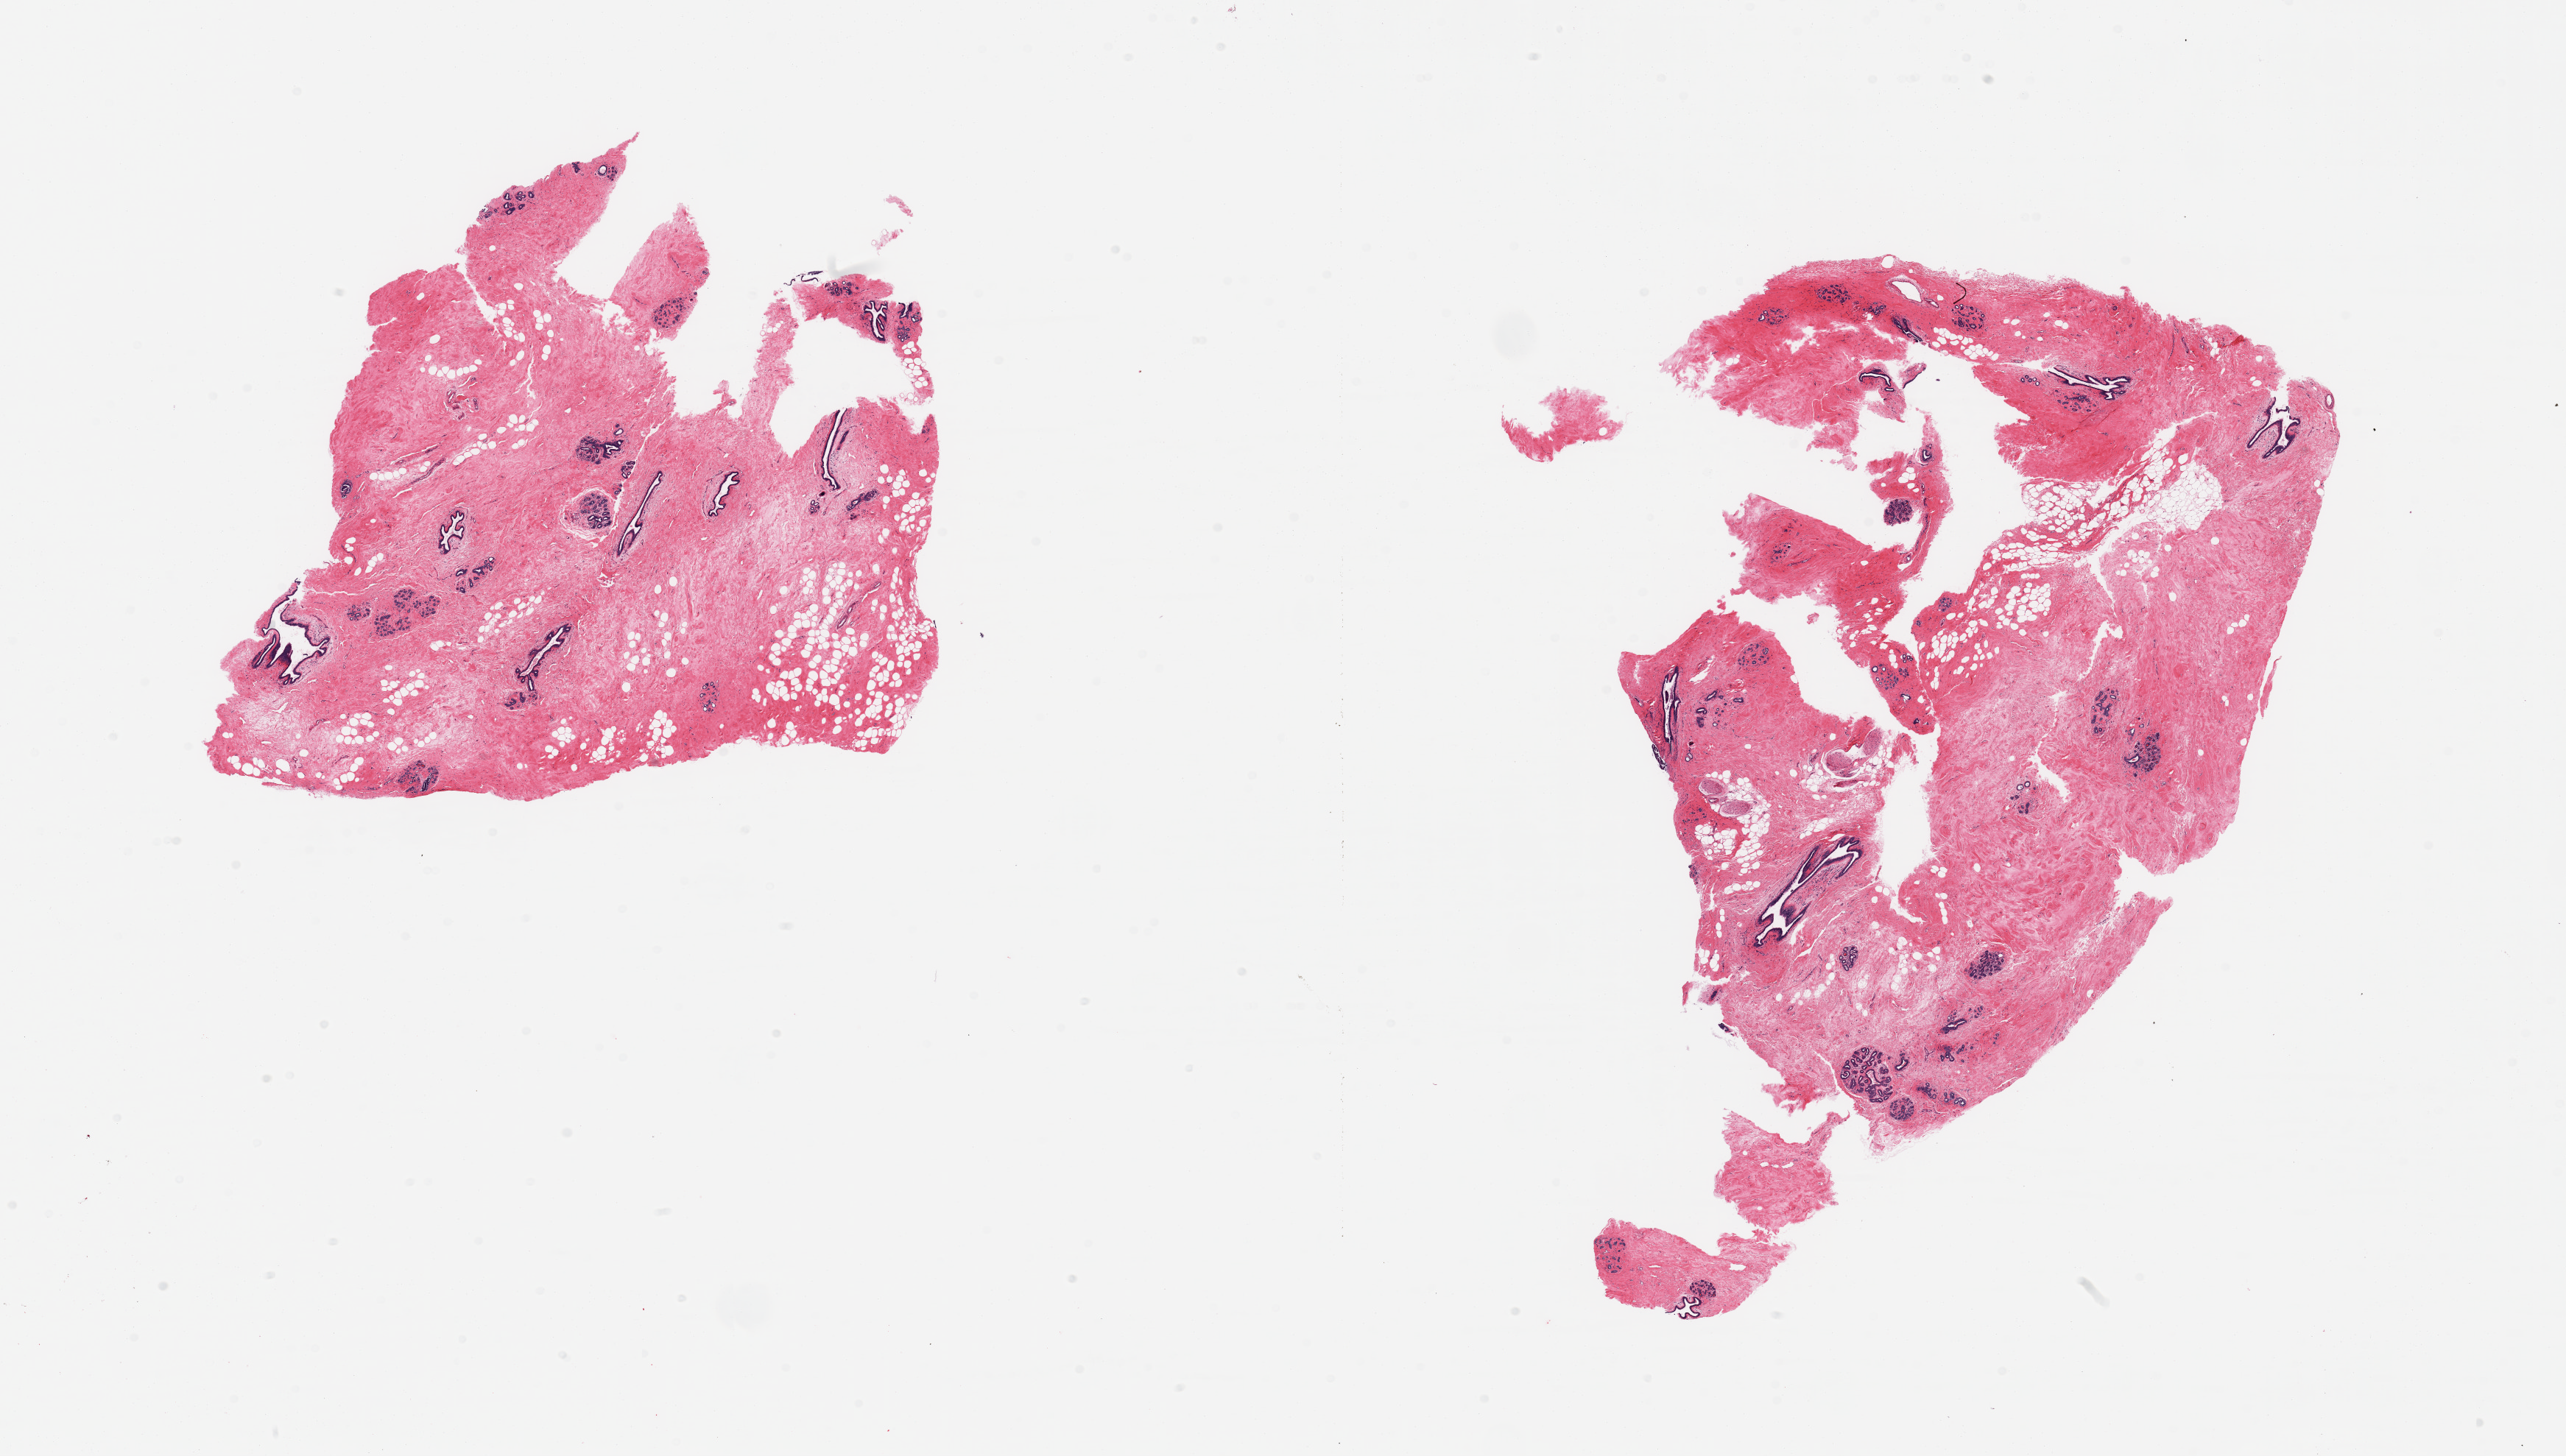
Haematoxylin and eosin whole-slide image — shown as a low-resolution overview of the whole scanned area (about 27.6 x 15.6 mm, slide scanned at 20x), PAXgene-fixed paraffin-embedded (PFPE) section, target tissue: breast, donor tissue sample.
Pathologist's review note for this sample: 2 pieces; lobular and ductal elements in predominantly fibrous stroma; 10% fat content.